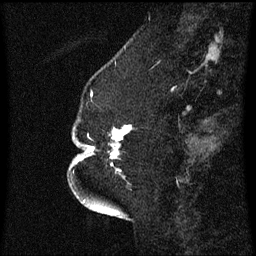
Breast MRI (dynamic contrast-enhanced), one sagittal slice; position 19 of 60 along the scan axis; dynamic contrast-enhanced series, image 2 of 3 at this slice position (ordered by acquisition); 1.5 T; TE 4.2 ms, TR 8.4 ms; 2.3 mm slice thickness; 256 × 256 image matrix. Female patient, age 52 years. From the clinical record (not read from this slice): setting: breast cancer imaged before/during neoadjuvant chemotherapy; receptor status: HR-positive, HER2-negative.
Annotated regions visible in this slice (semi-automatically segmented with operator editing):
- analysis volume of interest (the breast-tissue region the enhancement analysis was run in; not a lesion): box from (x=75, y=118) to (x=130, y=179) px
- tumour enhancement mask (voxels above the 70 % enhancement threshold inside the analysis volume of interest): (x=78, y=126)–(x=130, y=173)